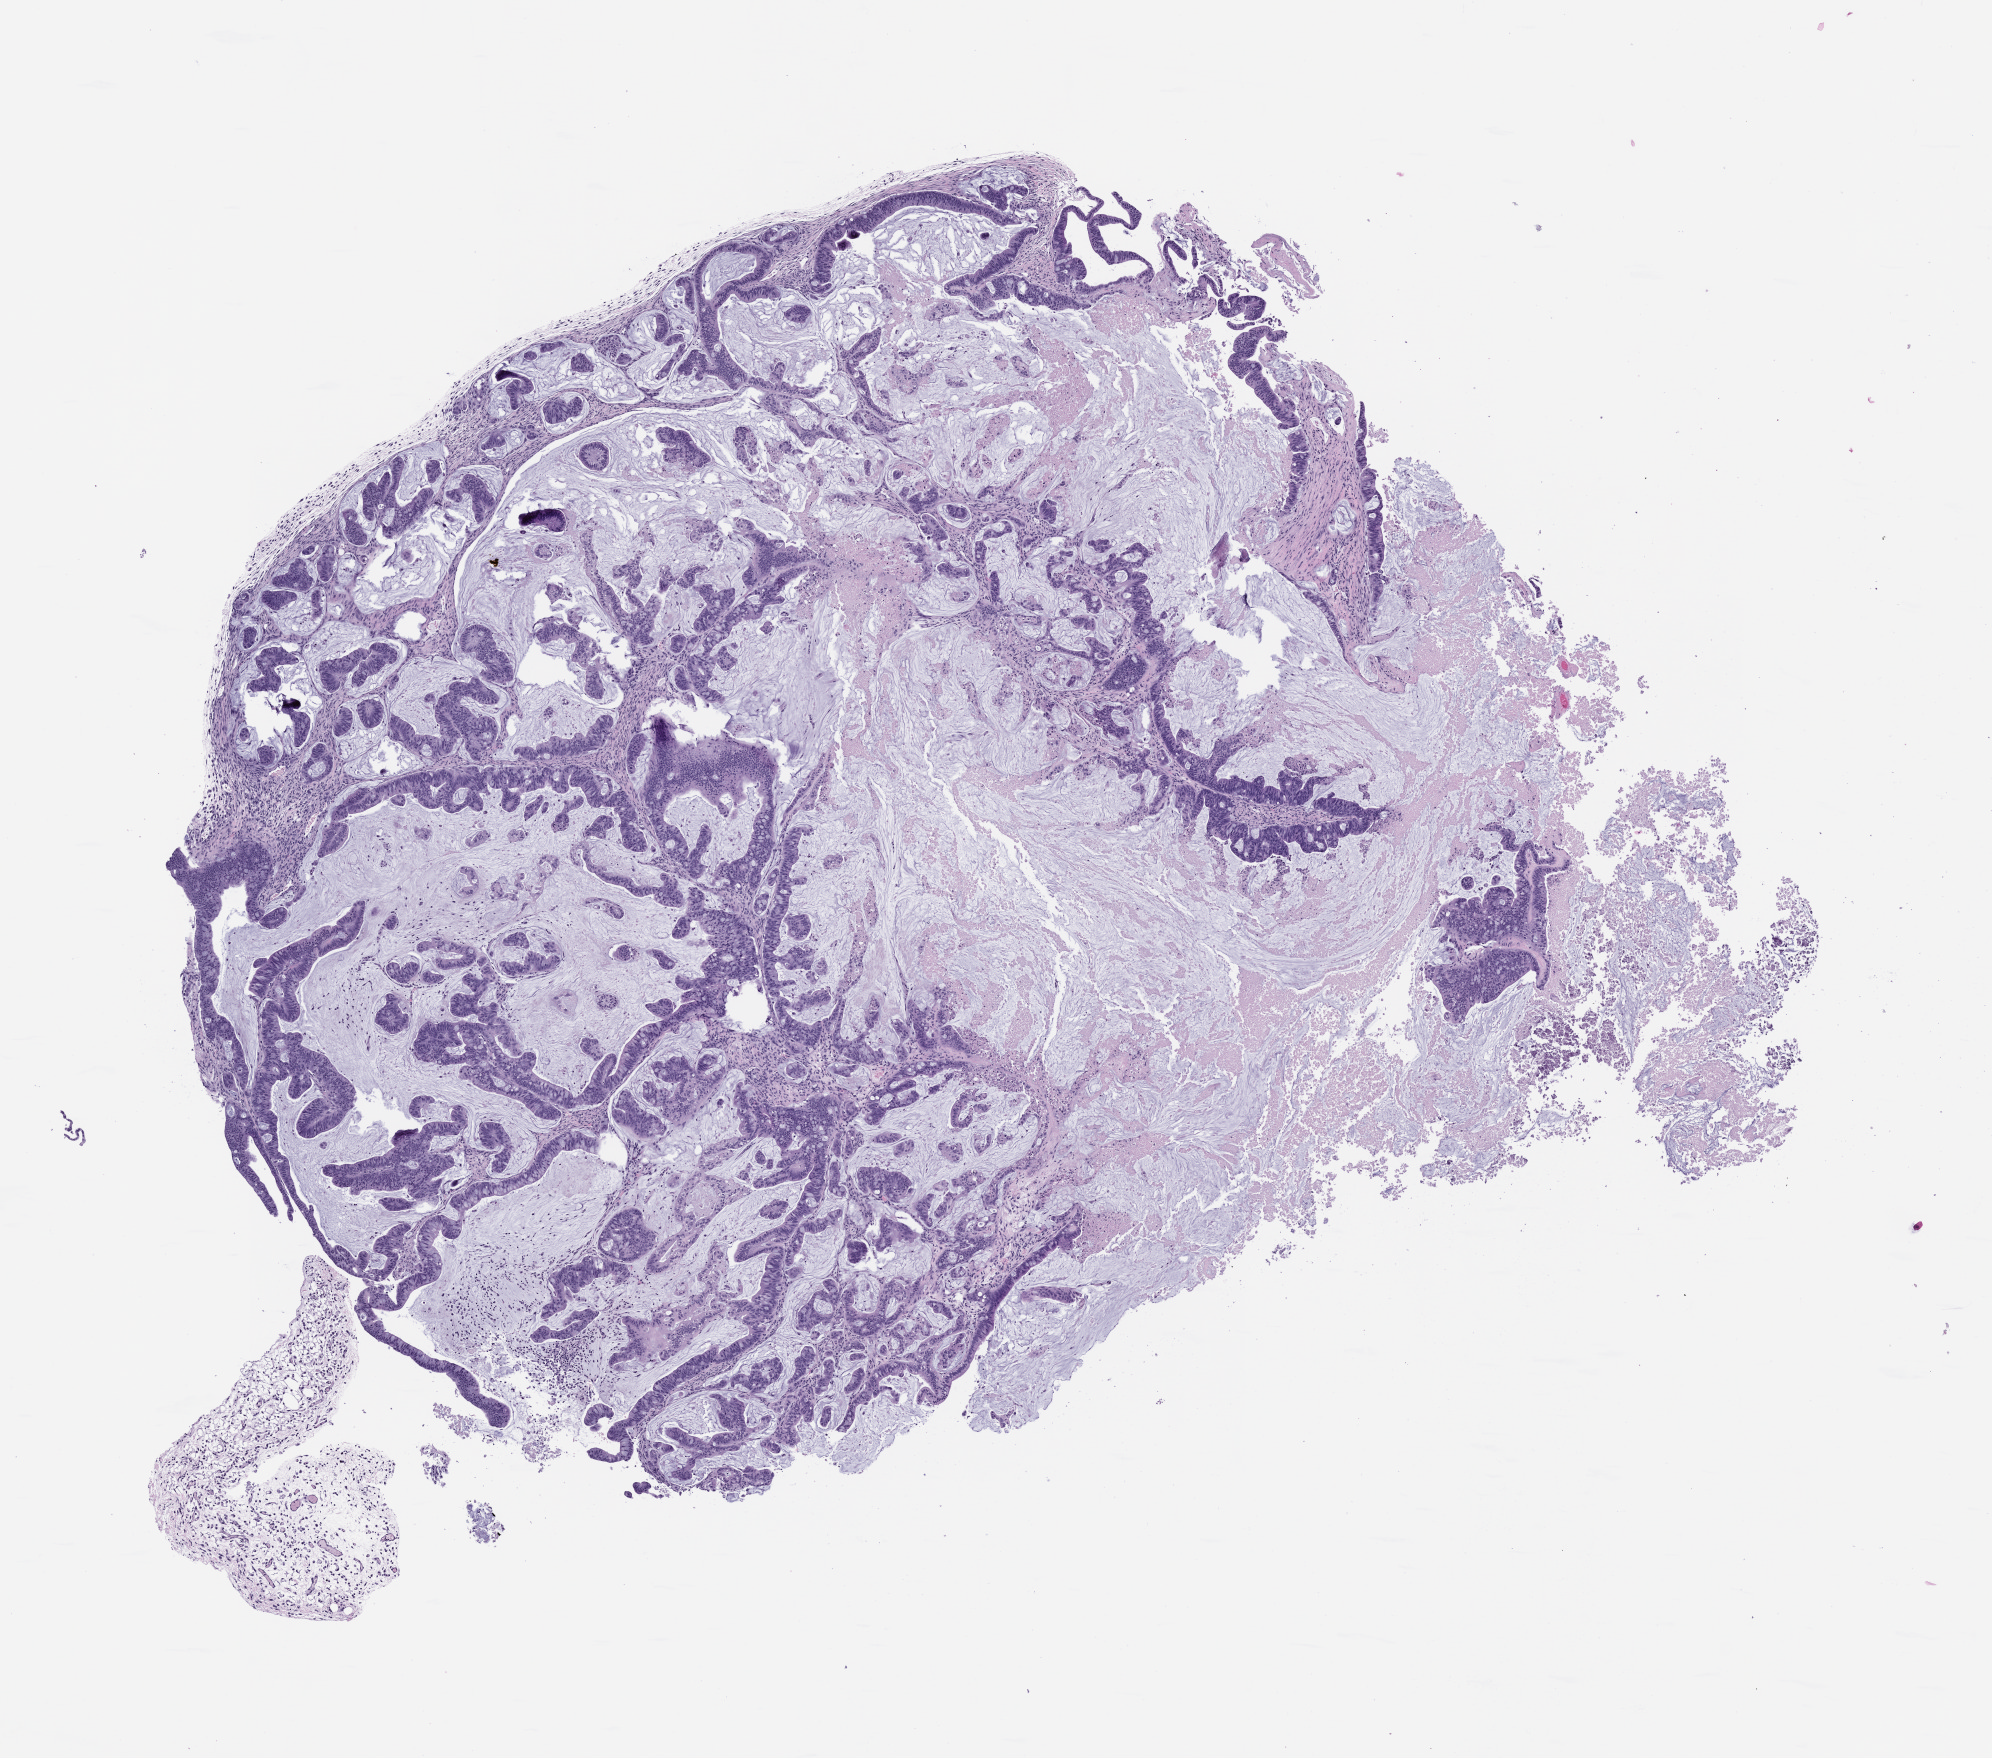
Hematoxylin and eosin (H&E) whole-slide image of a patient-derived xenograft (PDX) tumor grown in a mouse, passage 0, low-resolution overview of the scanned area, about 8.0 x 7.1 mm; formalin-fixed, paraffin-embedded (FFPE) tissue; originating tumor site category: rectum.
Originating patient diagnosis: Rectal Adenocarcinoma.